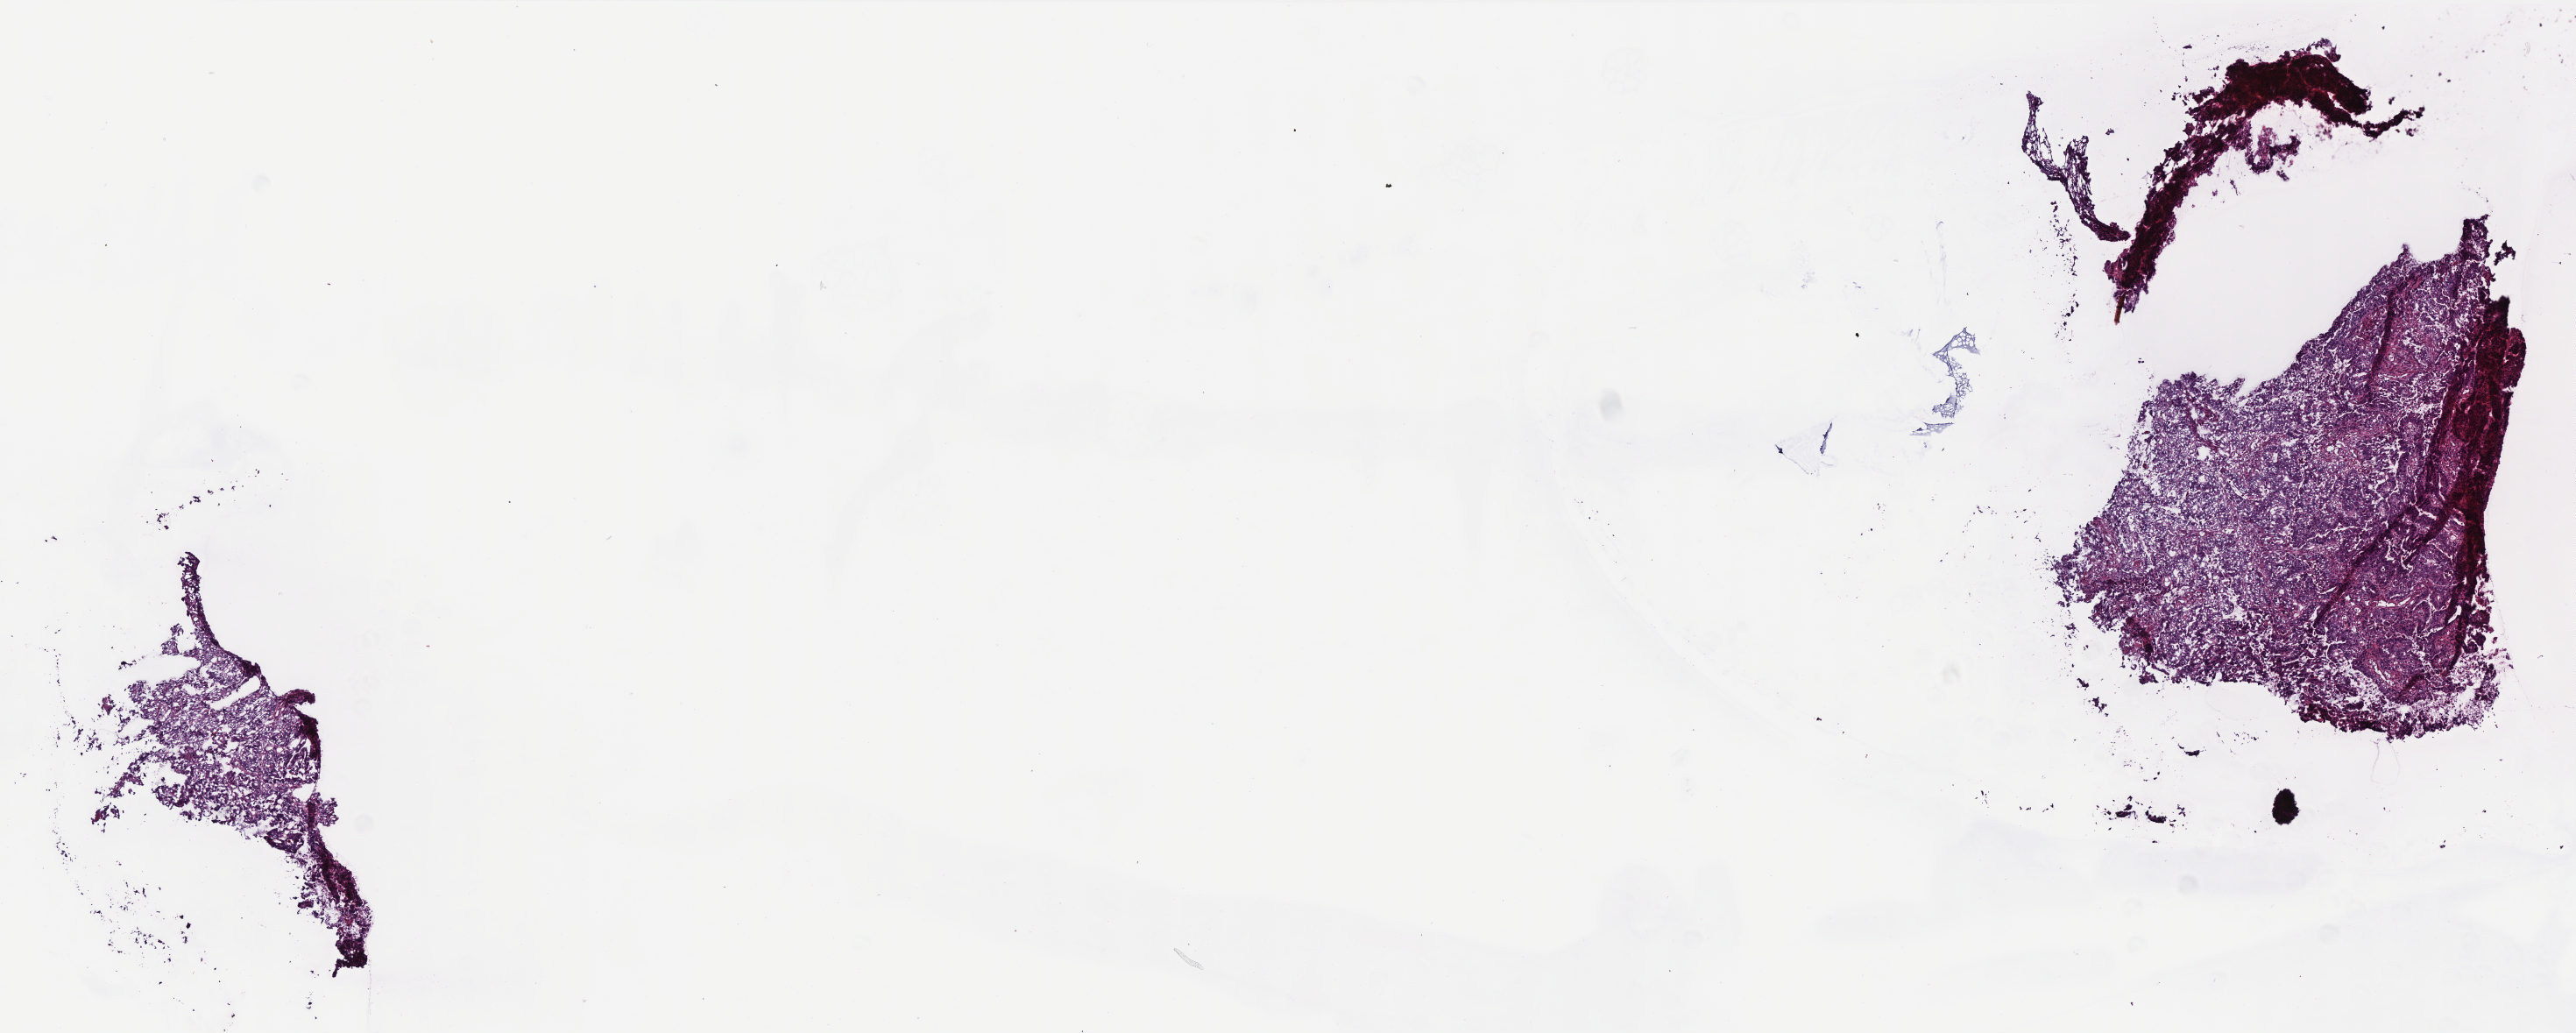
Digitized H&E-stained tissue section (whole slide) — low-resolution overview of the scanned area, about 11.8 x 4.7 mm (acquisition: 40x scan), frozen section from the bottom of the tissue portion, rectum, primary tumour sample. Male, age 86 years at initial diagnosis. Composition of this section per pathologist review: tumour cells 95%, tumour nuclei 90%, normal cells 0%, stromal cells 4%, necrosis 1%. Infiltration values recorded for this section: lymphocyte infiltration 4%, monocyte infiltration 1%, neutrophil infiltration 2%.
• TNM: T2 N0 M0
• AJCC pathologic stage: I
• histologic diagnosis: Adenocarcinoma, NOS